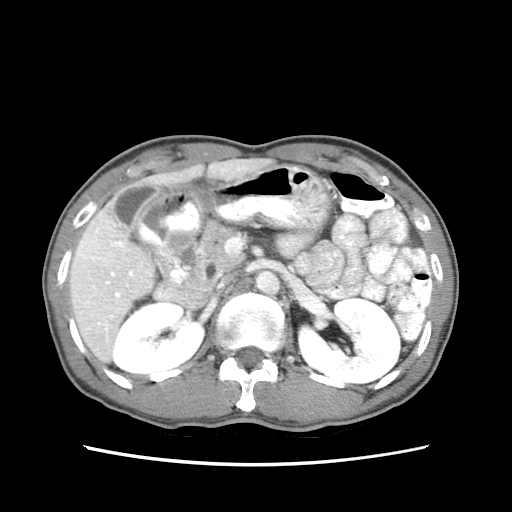
Contrast-enhanced abdominal CT (liver protocol), one axial slice. Slice 30 of 79 in the series (ordered by position). Reconstruction kernel STANDARD. Soft-tissue window (W 400 / L 40 HU). 2.5 mm slice thickness. 512 × 512 image matrix. From the clinical record (not read from this slice): diagnosis: hepatocellular carcinoma (patient treated with transarterial chemoembolisation; whether this scan precedes or follows treatment is not stated here); TNM stage (as recorded): Stage-IIIB; Child-Pugh class: A; tumour differentiation: moderately differentiated; tumour nodularity: multinodular.
Outlined on this slice (semi-automatic segmentation, software-assisted and operator-edited):
- liver parenchyma outside the tumour (the mass and vessels are separate outlines, so this box may not span the whole liver): bounding box (x1, y1, x2, y2) in pixels: (68, 156, 274, 360)
- liver vessels: (79, 167, 225, 324)